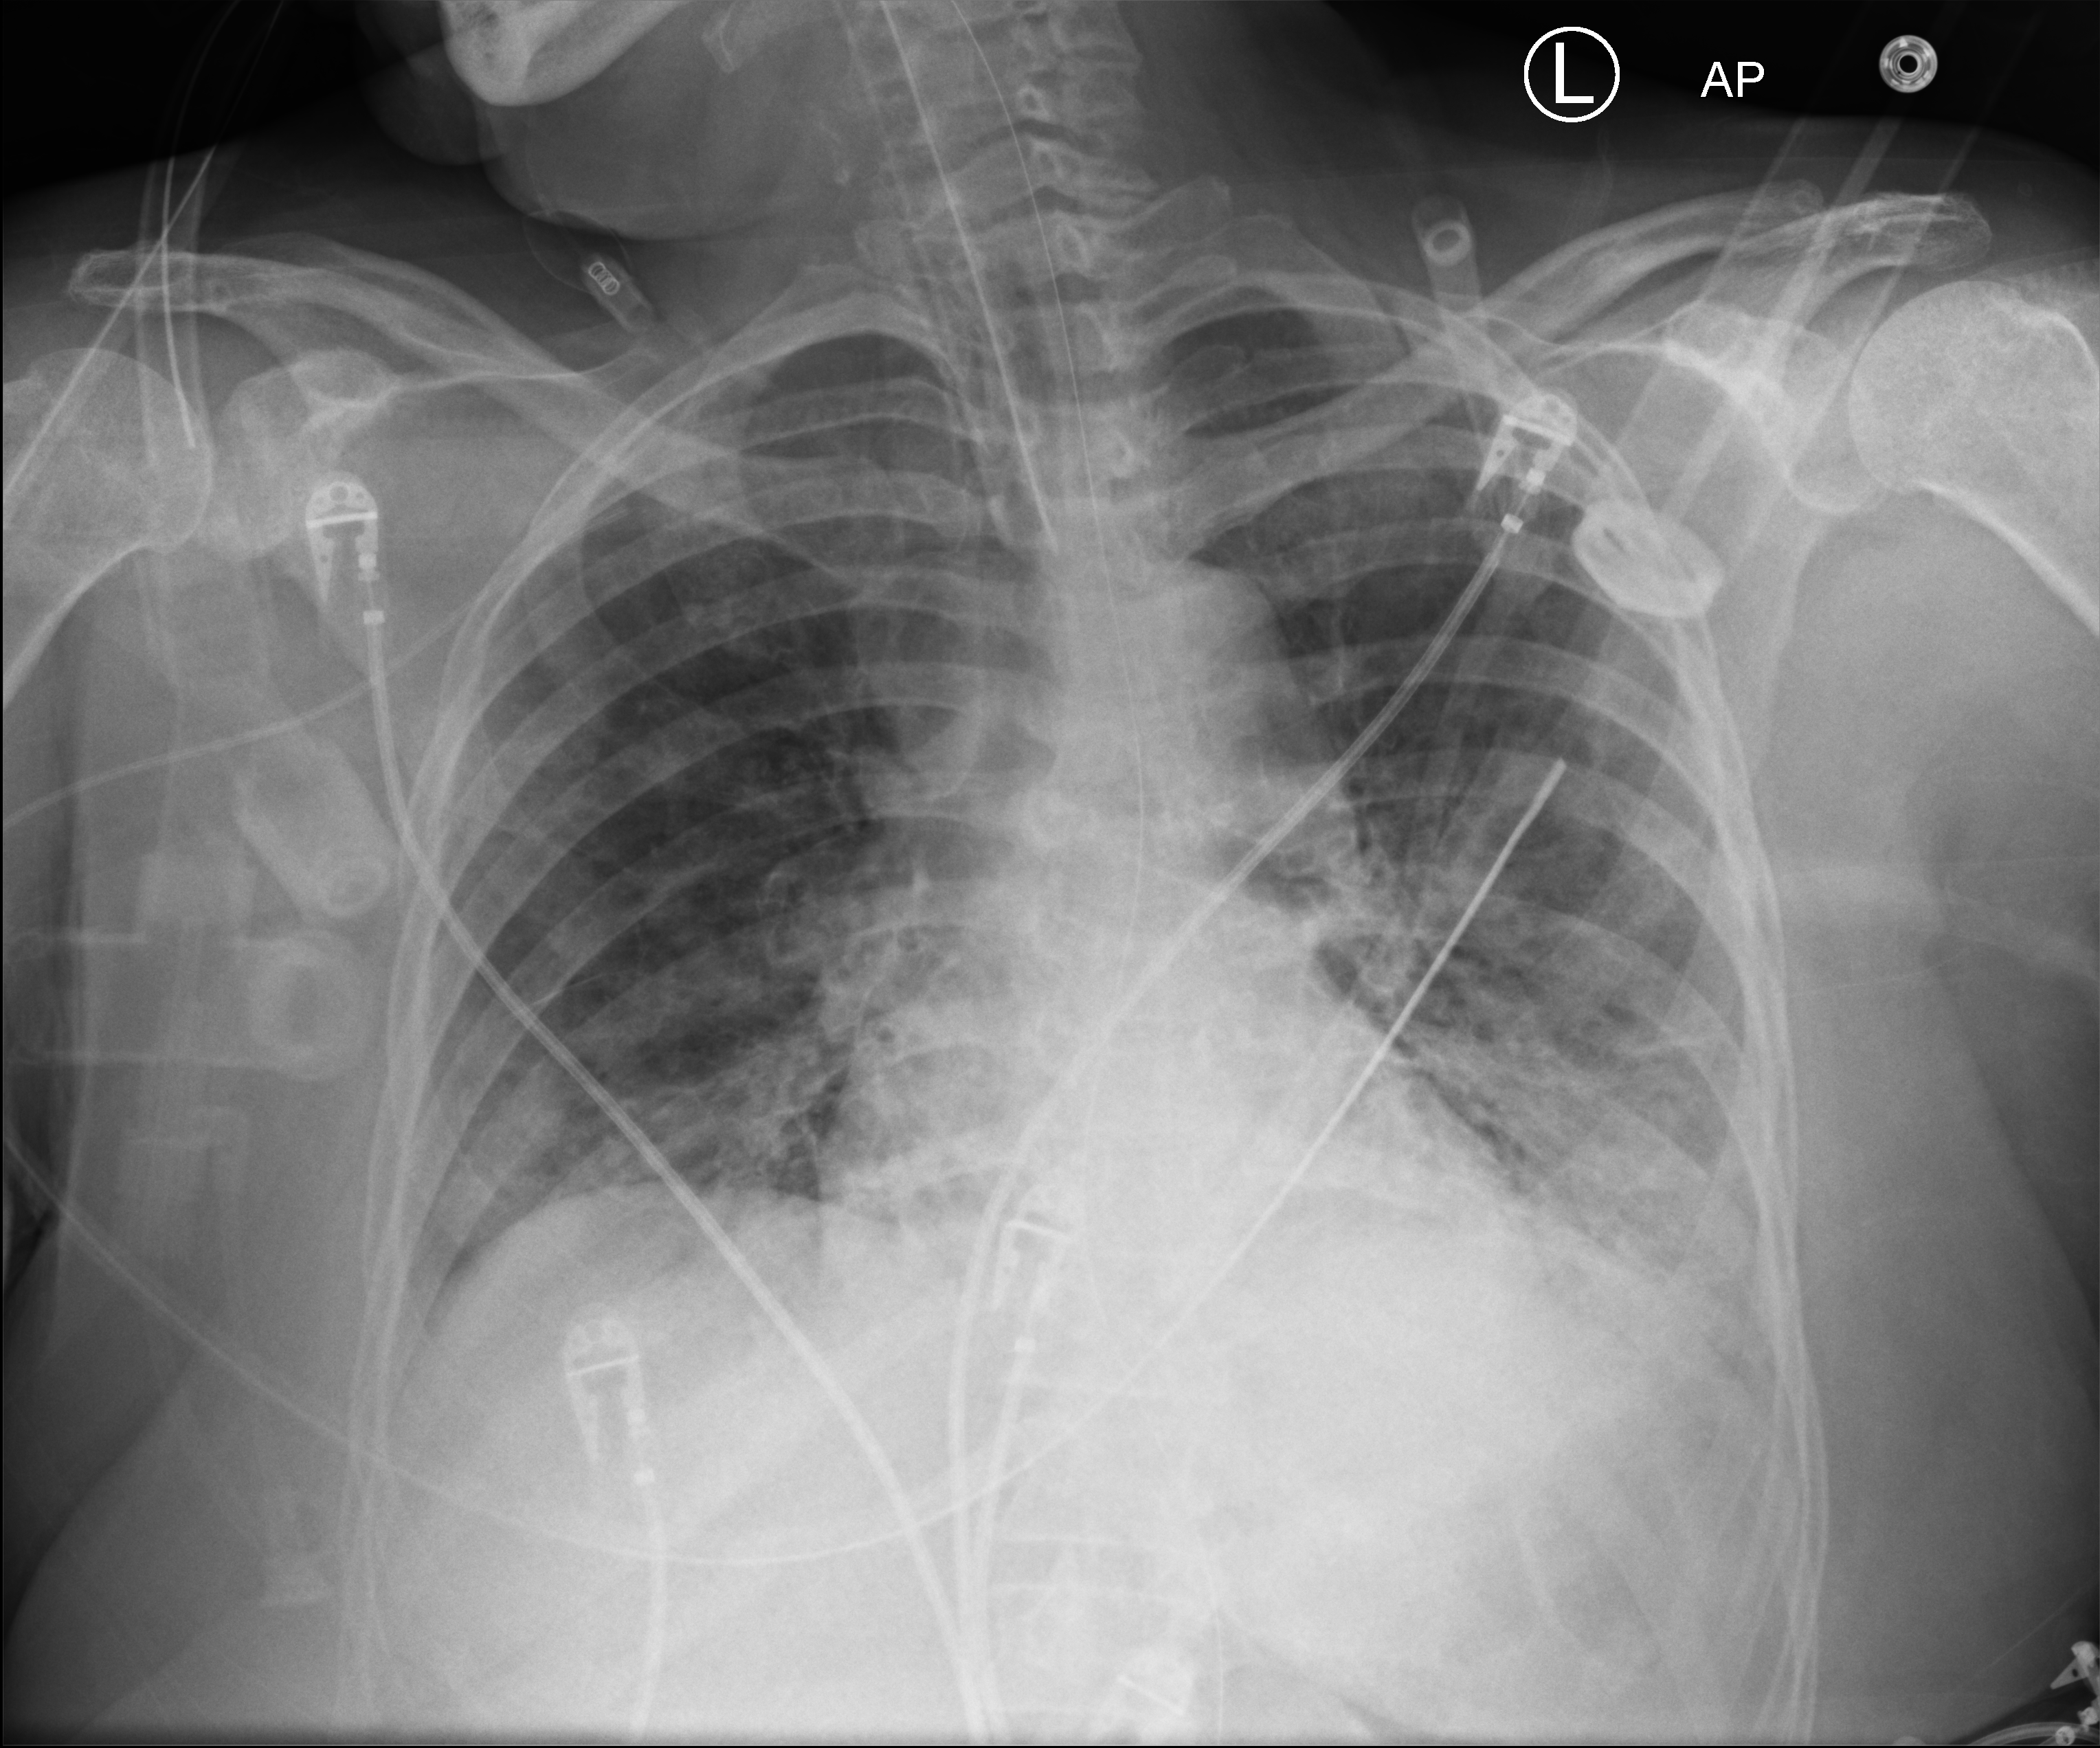
Portable chest radiograph, anteroposterior (AP) projection. Patient hospitalised with COVID-19; female, aged 75–90 years.
Hospital-stay facts (about this admission, not read from this image; timing relative to this image not recorded): admitted to intensive care during this hospital stay: yes.